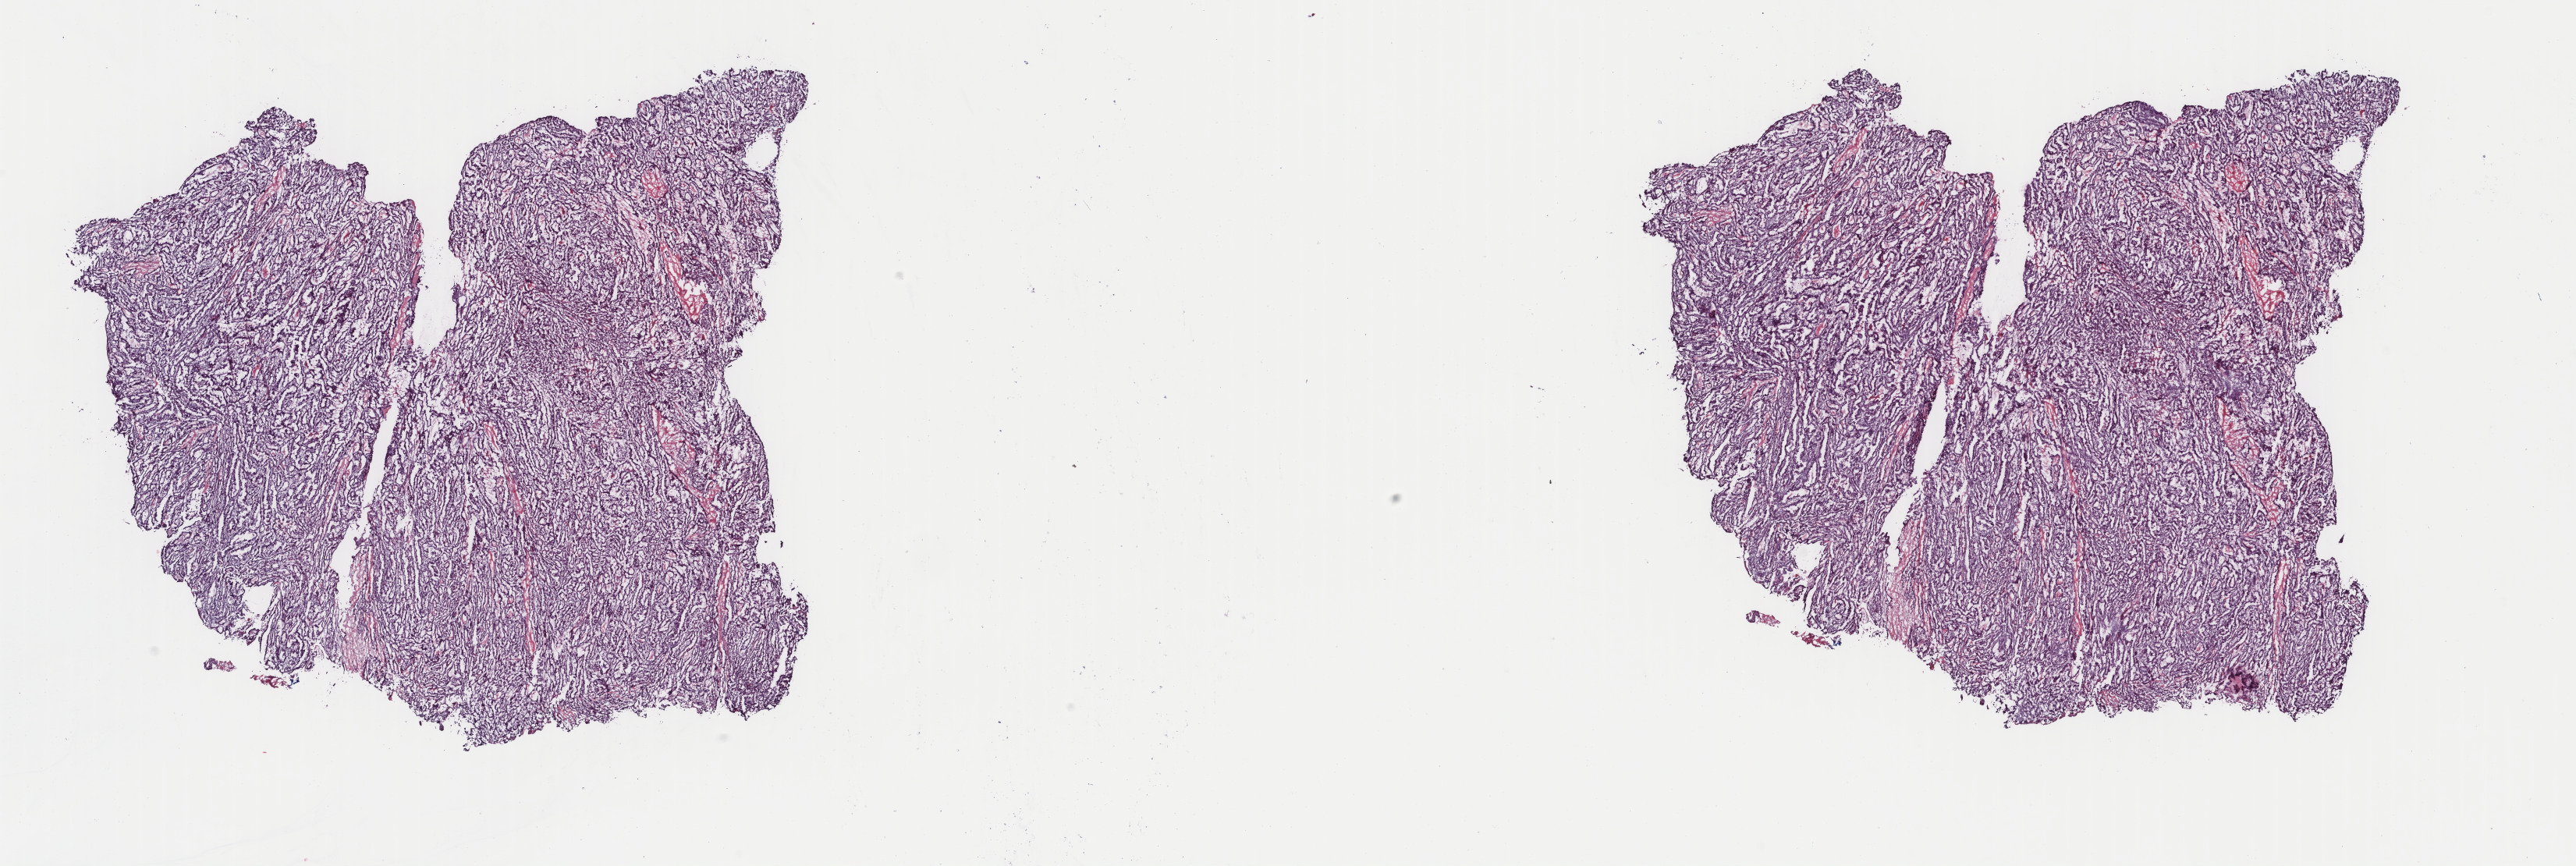
Hematoxylin and eosin (H&E) stained whole-slide image — low-resolution overview of the scanned area, about 26.2 x 8.8 mm (from a 40x scan), frozen section from the top of the tissue portion, sample: primary tumour, thyroid. Female, age 43 years at initial diagnosis. Composition of this section per pathologist review: tumour cells 95%, tumour nuclei 100%, normal cells 0%, stromal cells 5%, necrosis 0%. Inflammatory infiltration, as recorded: lymphocyte infiltration 3%, monocyte infiltration 2%, neutrophil infiltration 0%.
* TNM: T3 N1b M0
* pathologic diagnosis: Papillary adenocarcinoma, NOS
* laterality: right
* lymph nodes positive (case pathology): 1 of 1 examined
* AJCC pathologic stage: I